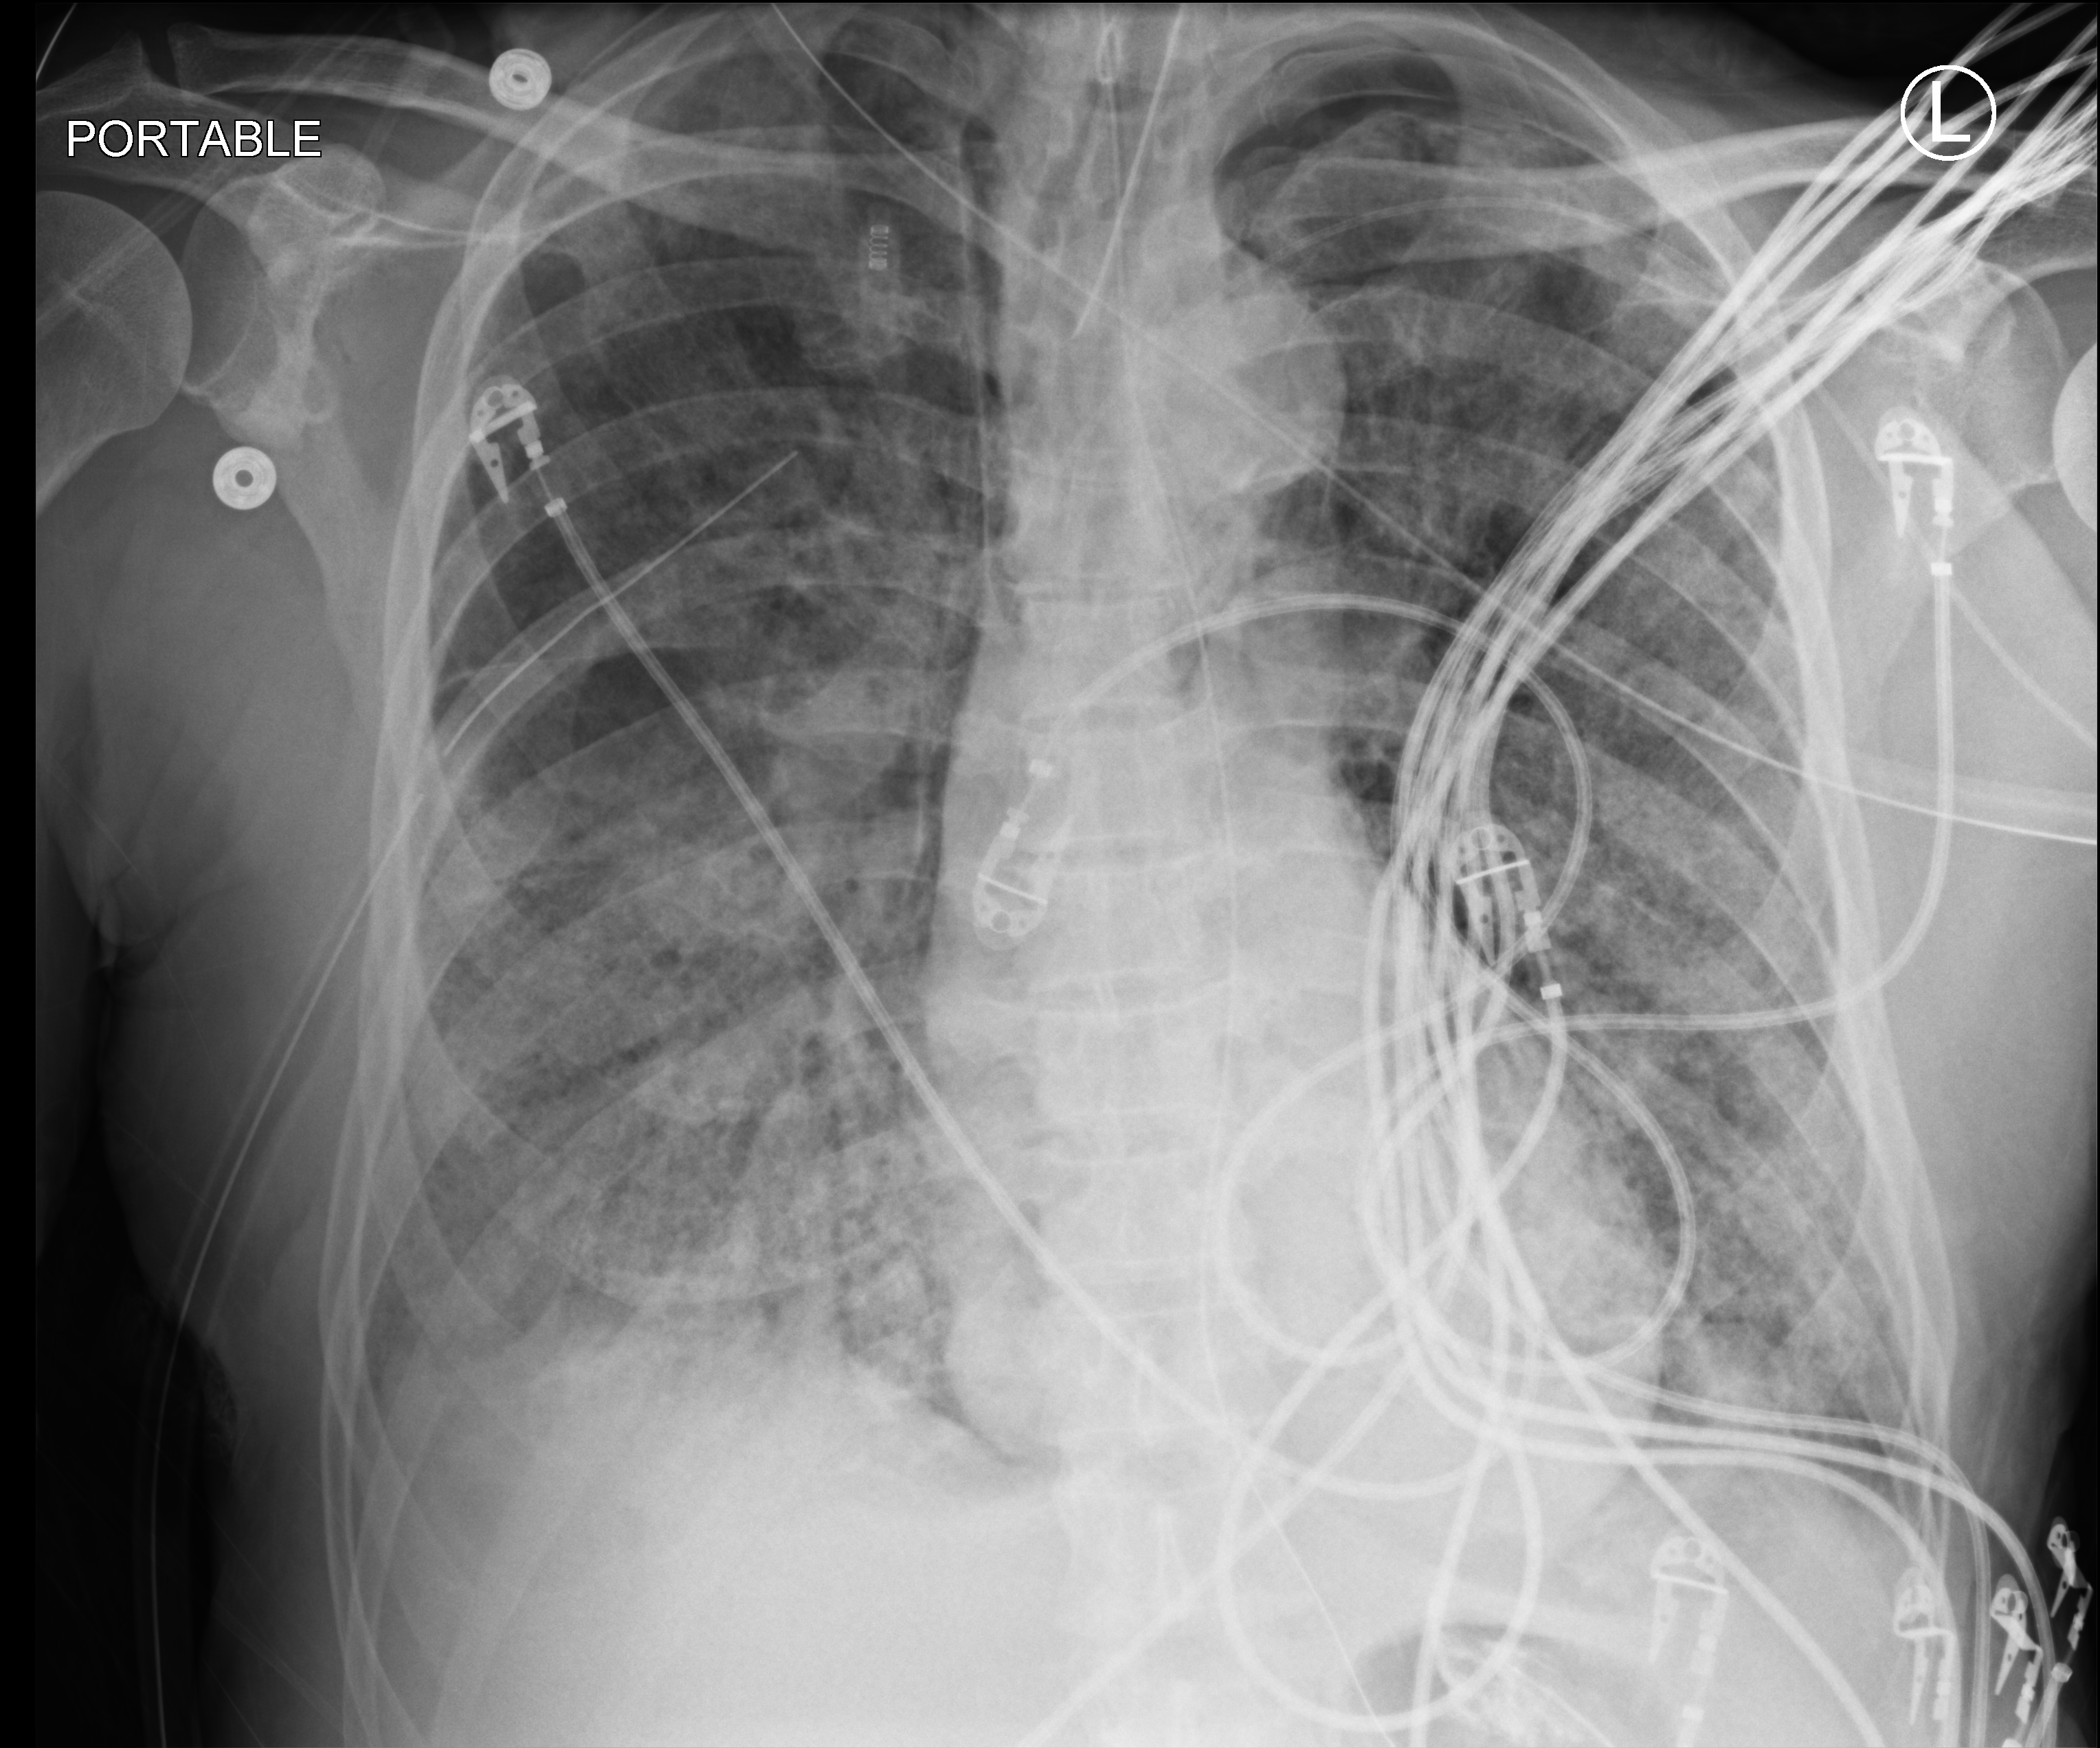
Chest X-ray (portable), anteroposterior (AP) projection. Male patient hospitalised with COVID-19, age 60–74 years.
From the hospital-stay record, not from the radiograph (when in the stay this image was taken is not recorded): smoking status (admission record): former; other chronic lung disease (admission record): no.